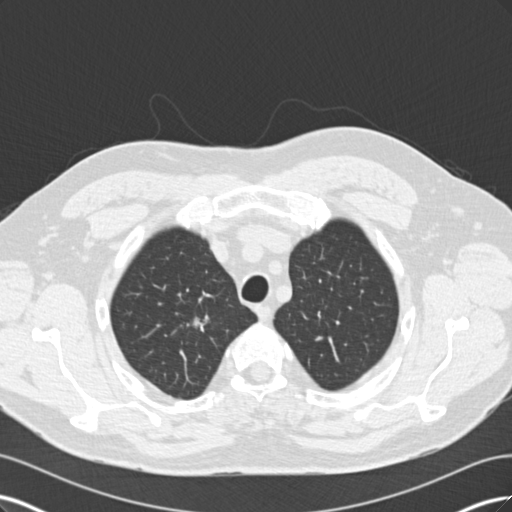
Low-dose screening chest CT, axial slice. Baseline annual screen. Lung window (W 1500 / L -600 HU). 2 mm slice thickness. Standard (soft-tissue) reconstruction kernel (B30f). Slice 27 of 171 in the series. 512 × 512 image matrix, field of view 360 × 360 mm. Male participant, aged 56 years at enrolment. Former smoker at enrolment.
Expert reader's lesion annotation, bounding box (x1, y1, x2, y2) in pixels: (172, 304, 228, 350). Screening reader's record for this exam (one nodule recorded; not confirmed to be the boxed lesion): non-calcified nodule or mass ≥4 mm, right upper lobe, 14 × 8 mm, spiculated (stellate) margins. Lung cancer was diagnosed 146 days after this screen: adenocarcinoma, NOS, right upper lobe, poorly differentiated (G3), stage IA (AJCC 6th edition), 12 mm at pathology.